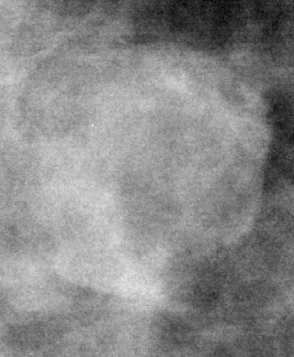
Cropped region of a digitized screen-film mammogram centred on a radiologist-marked abnormality; right breast; MLO view.
Mass, shape round, margins circumscribed; BI-RADS assessment category 3; pathology result (as recorded, not read from the image): benign.